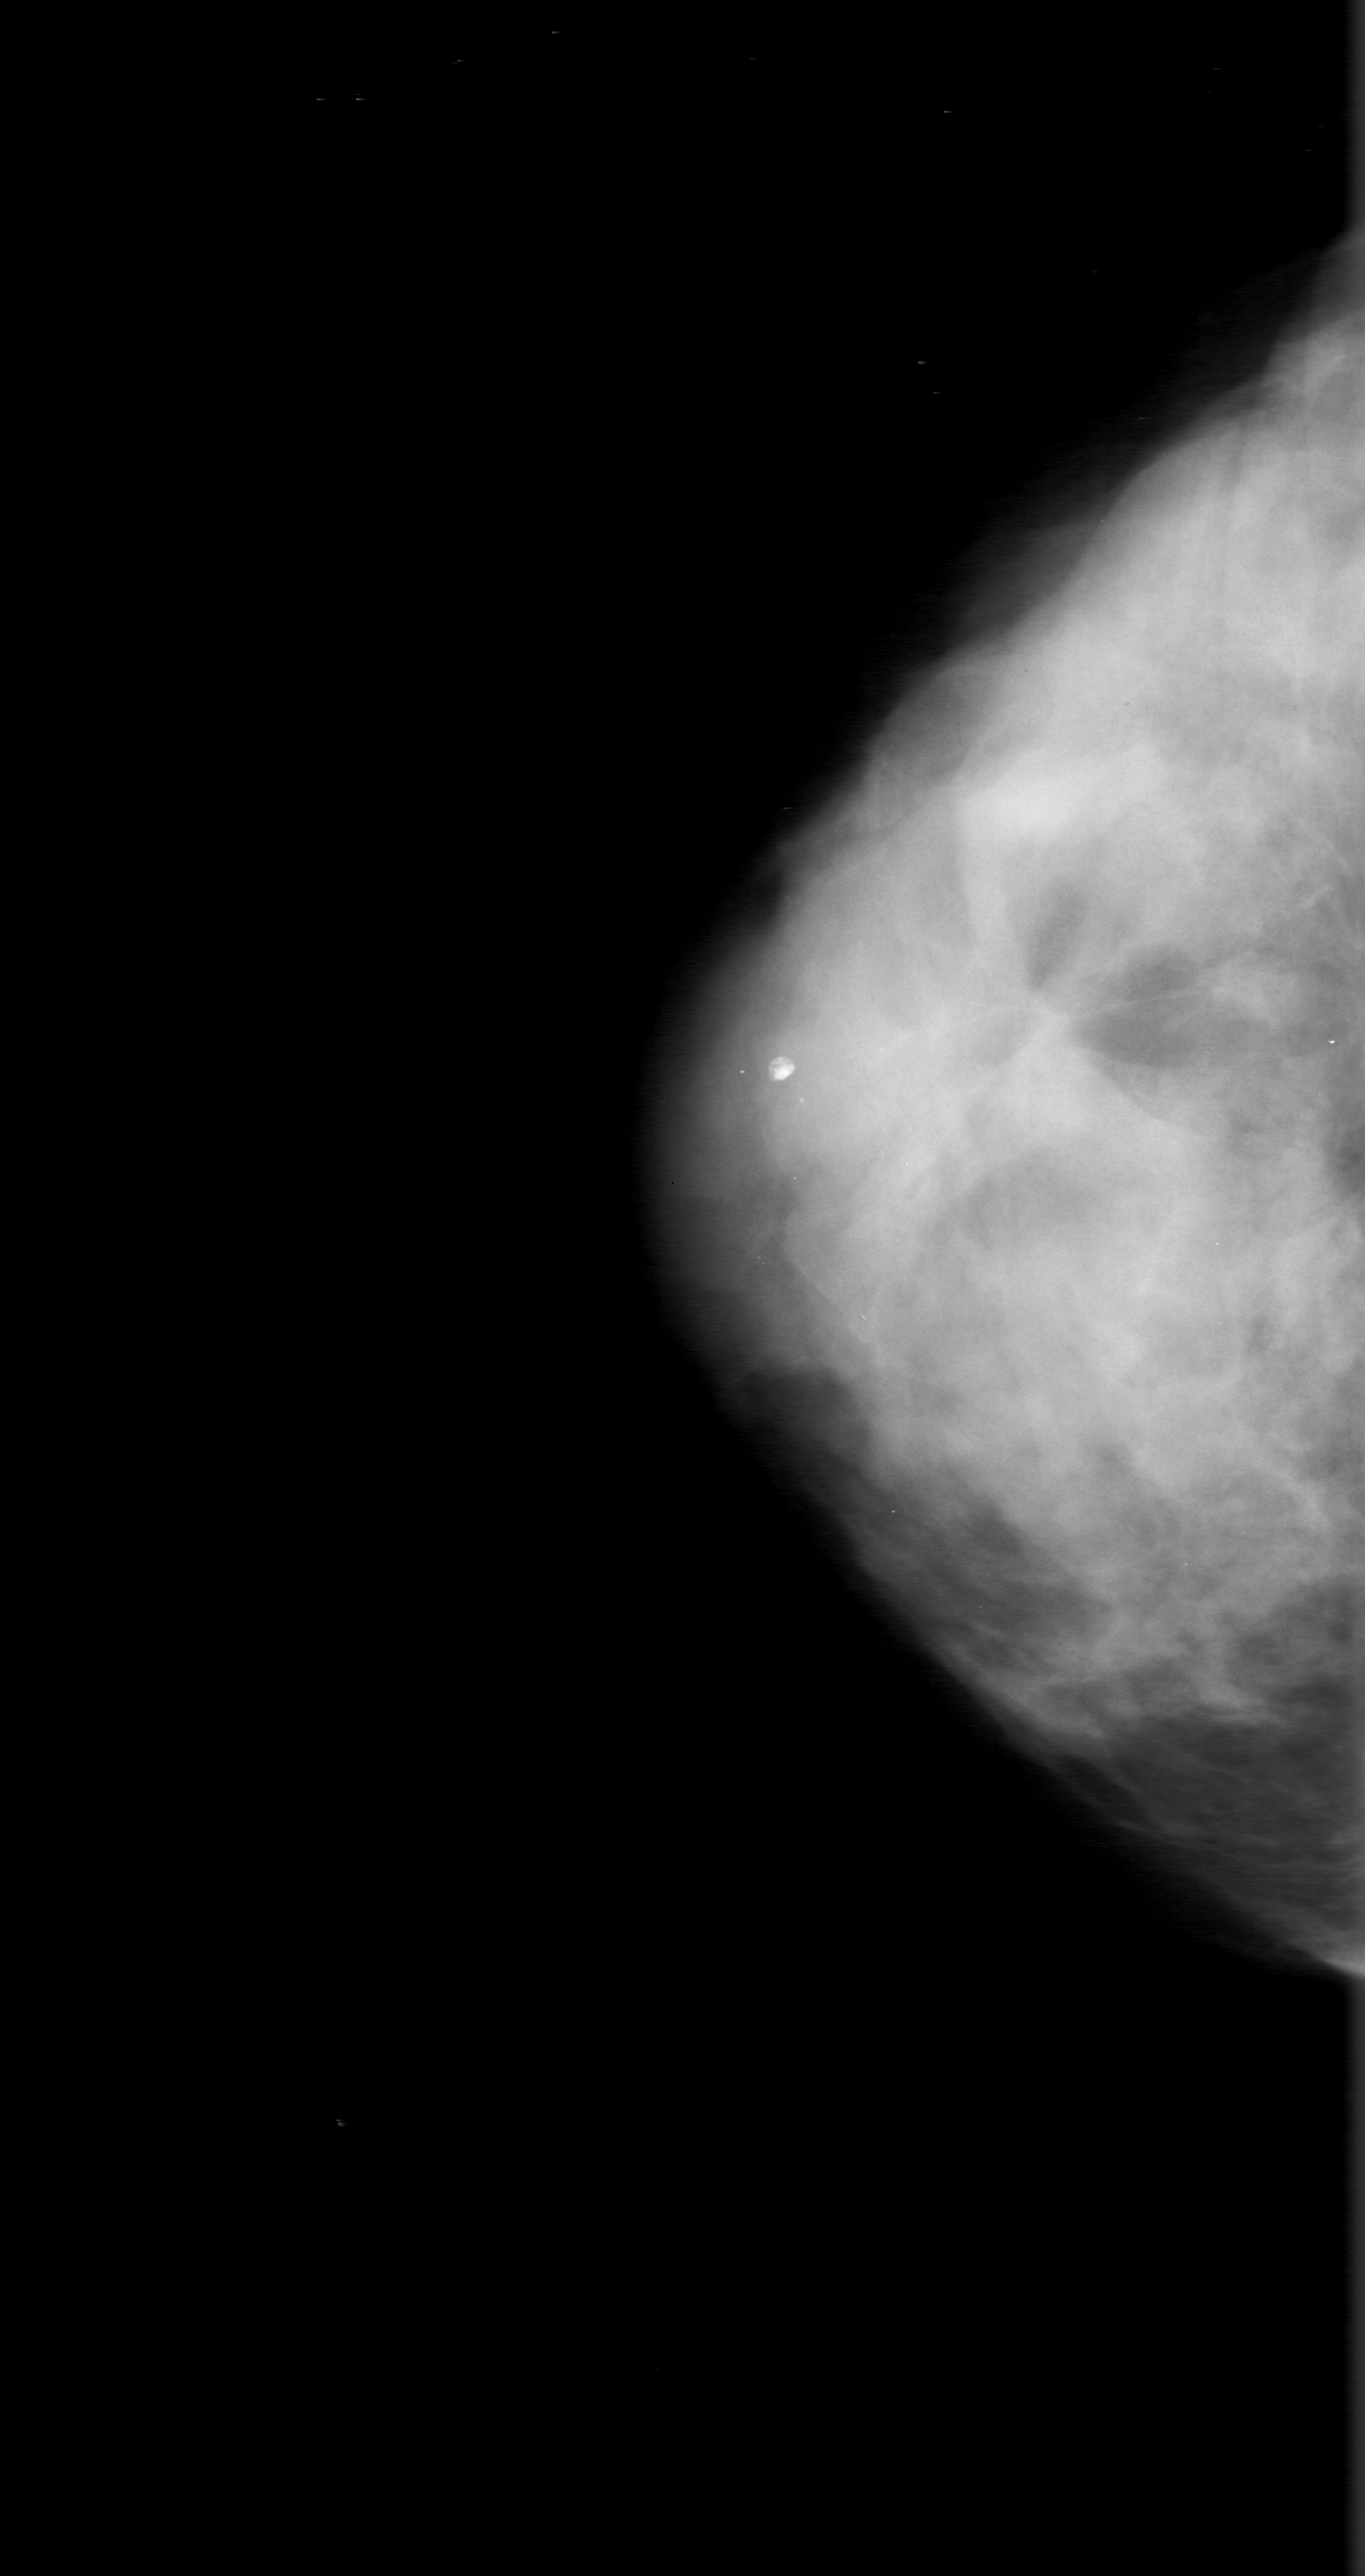
Digitized screen-film mammogram; right breast; craniocaudal (CC) view; breast composition: extremely dense (BI-RADS density category 4 of 4); 1365 × 2576 image matrix.
Expert-marked regions of interest on this image (one box per marked abnormality):
- mass, shape architectural distortion; BI-RADS assessment category 5; pathology (as recorded): malignant: bounding box (x1, y1, x2, y2) in pixels: (901, 924, 1172, 1198)